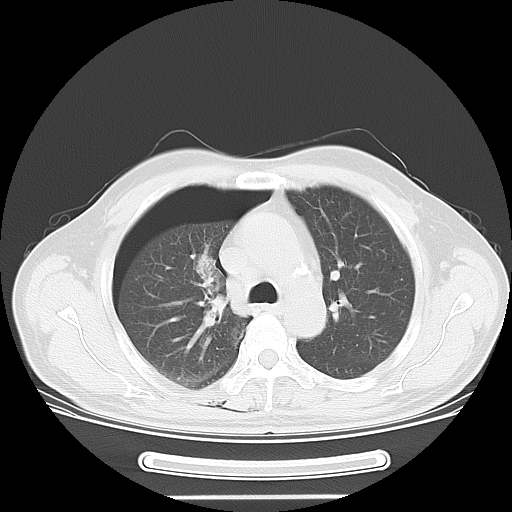
Chest CT, one axial slice; slice 40 of 57 in the series (ordered by position); reconstruction kernel LUNG; lung window (W 1500 / L -600 HU); 5 mm slice thickness; 512 × 512 image matrix, field of view 376 × 376 mm. Male patient, age 61 years. Case-level facts recorded for this patient, not image findings: clinical TNM (as recorded): T1c N3 M1b.
Outlined on this slice (rectangle marked by the reading radiologist):
- lung tumour (recorded histology: adenocarcinoma): box from (x=184, y=246) to (x=233, y=336) px